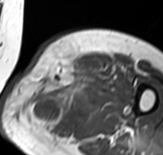
MRI of an extremity soft-tissue mass, one axial slice; slice 45 of 65 in the series (ordered by position); MR volume resampled by the dataset authors to the PET/CT grid (not the native acquisition matrix); 3.27 mm slice thickness; 163 × 155 image matrix. Female patient. From the clinical record (not read from this slice): histological type: pleomorphic leiomyosarcoma; grade: high; site of the primary tumour: left thigh.
Outlined on this slice (expert contour drawn on MRI and transferred to this co-registered scan by the dataset authors):
- gross tumour volume including surrounding oedema: box from (x=26, y=60) to (x=102, y=134) px
- gross tumour volume (mass): (x=67, y=85)–(x=84, y=96)